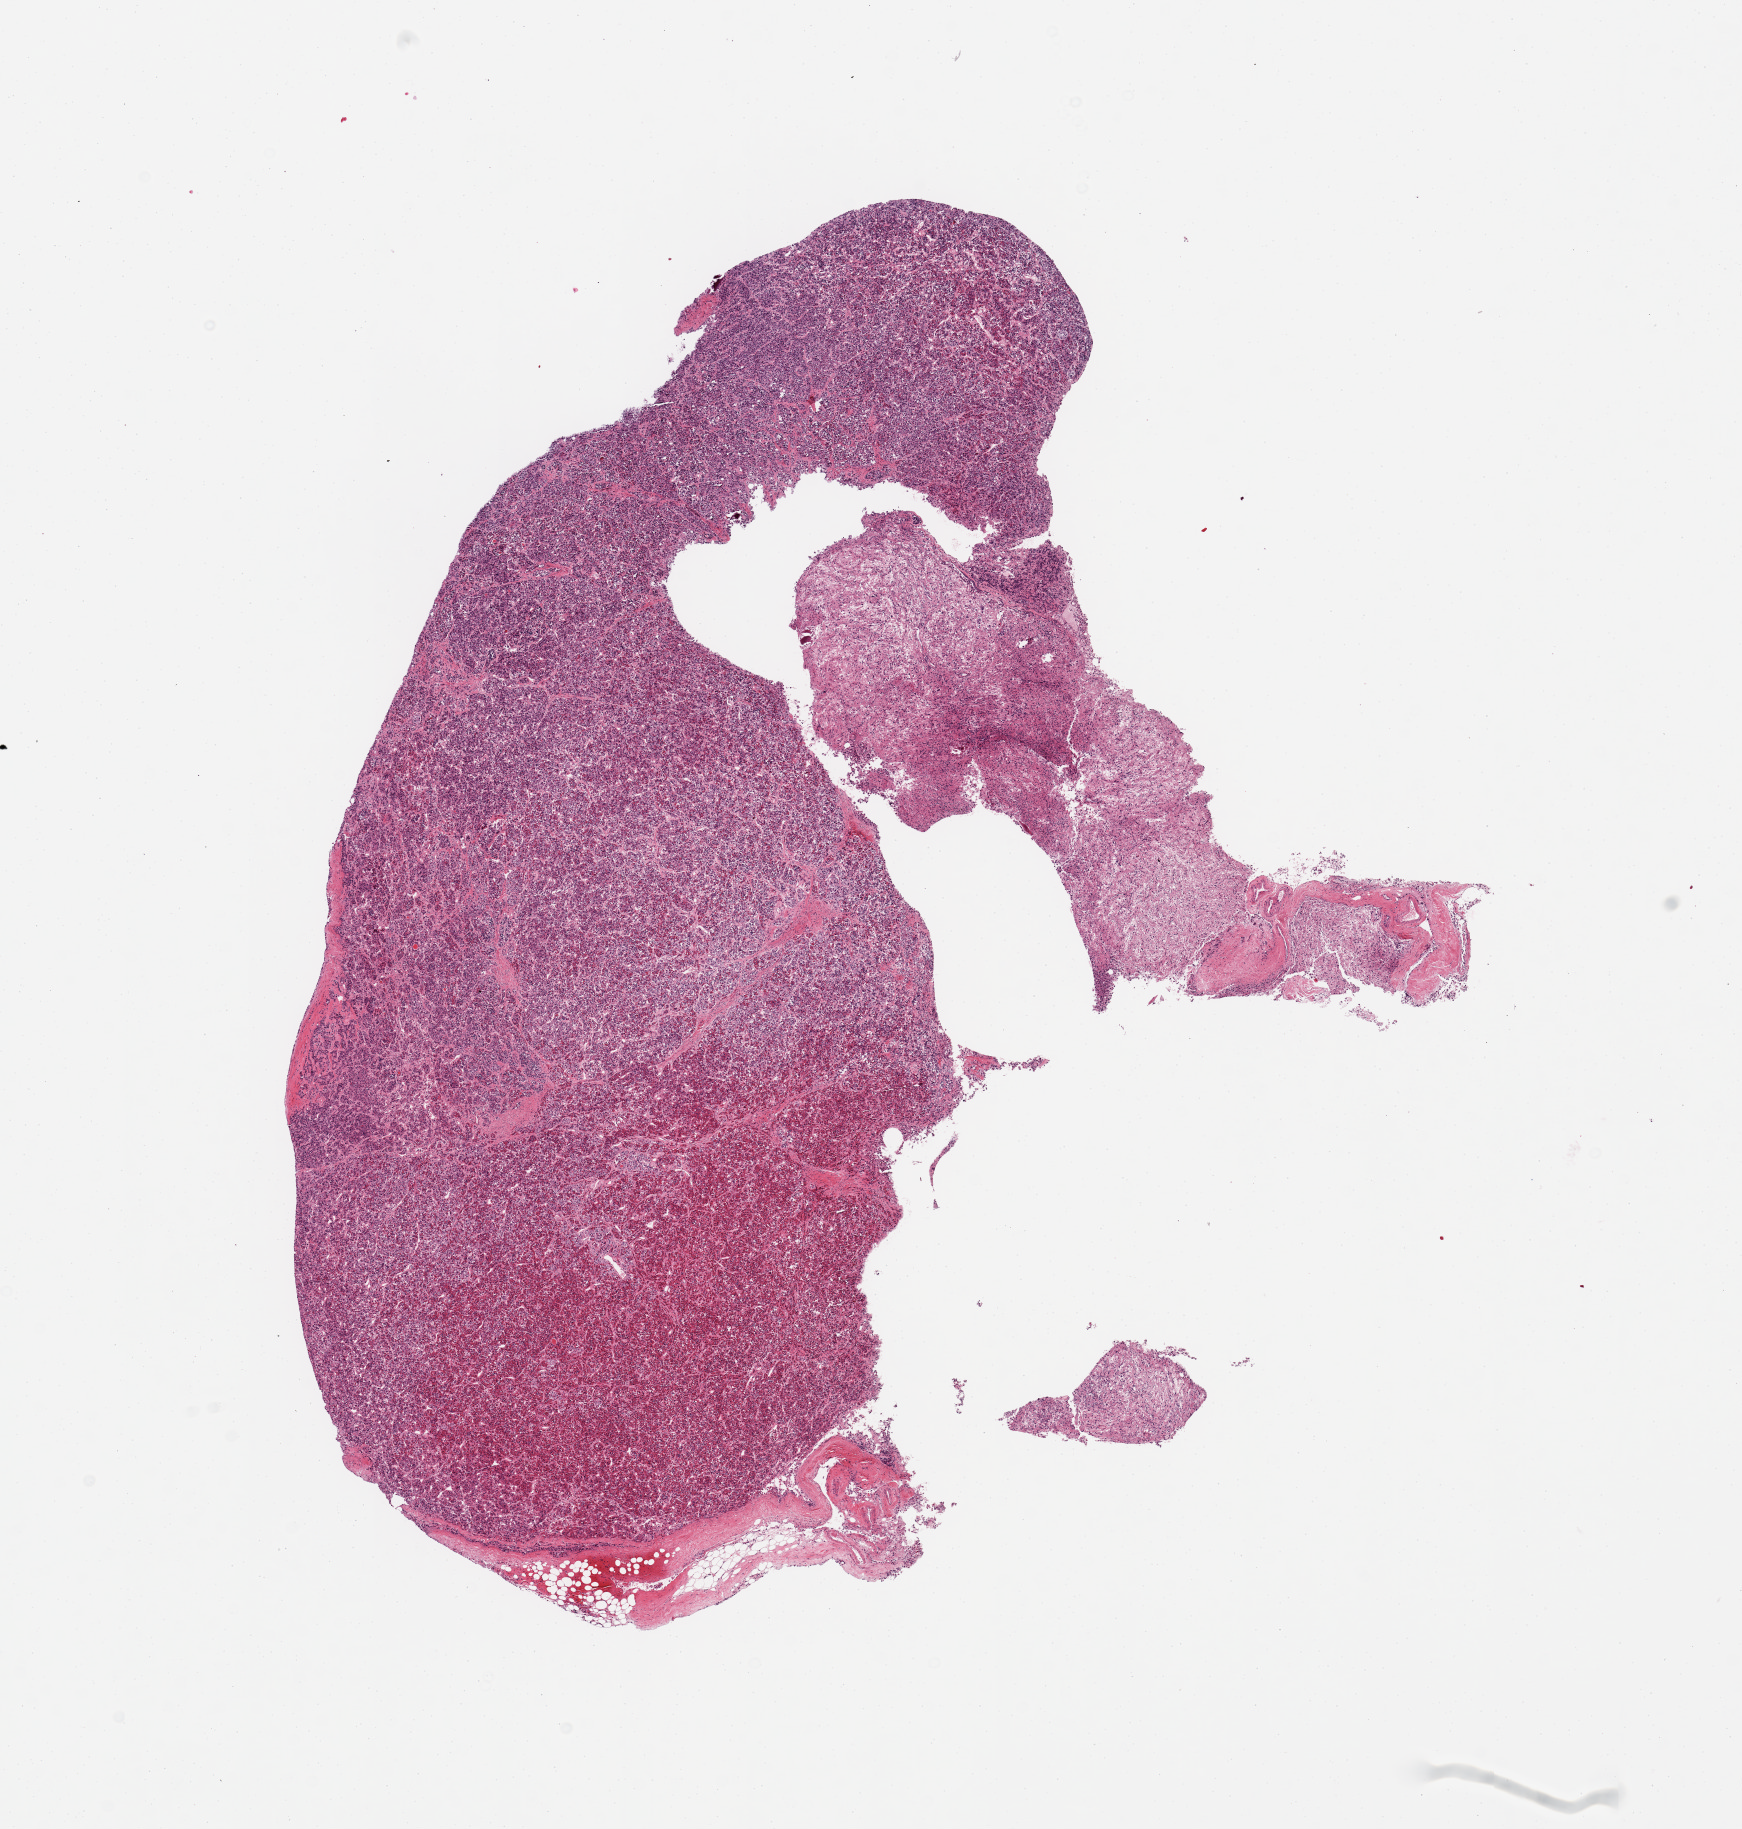
Whole-slide image, H&E stain — whole scanned area (about 13.8 x 14.5 mm, from a 20x scan) shown as a low-resolution overview, PAXgene-fixed paraffin-embedded (PFPE) section, section of pituitary (target tissue), tissue donor sample. Donor: male.
Reviewer comment on this tissue sample: 1piece (fragmented), mainly adenohypophysis, ~5mm fragment of neurohypophysis.